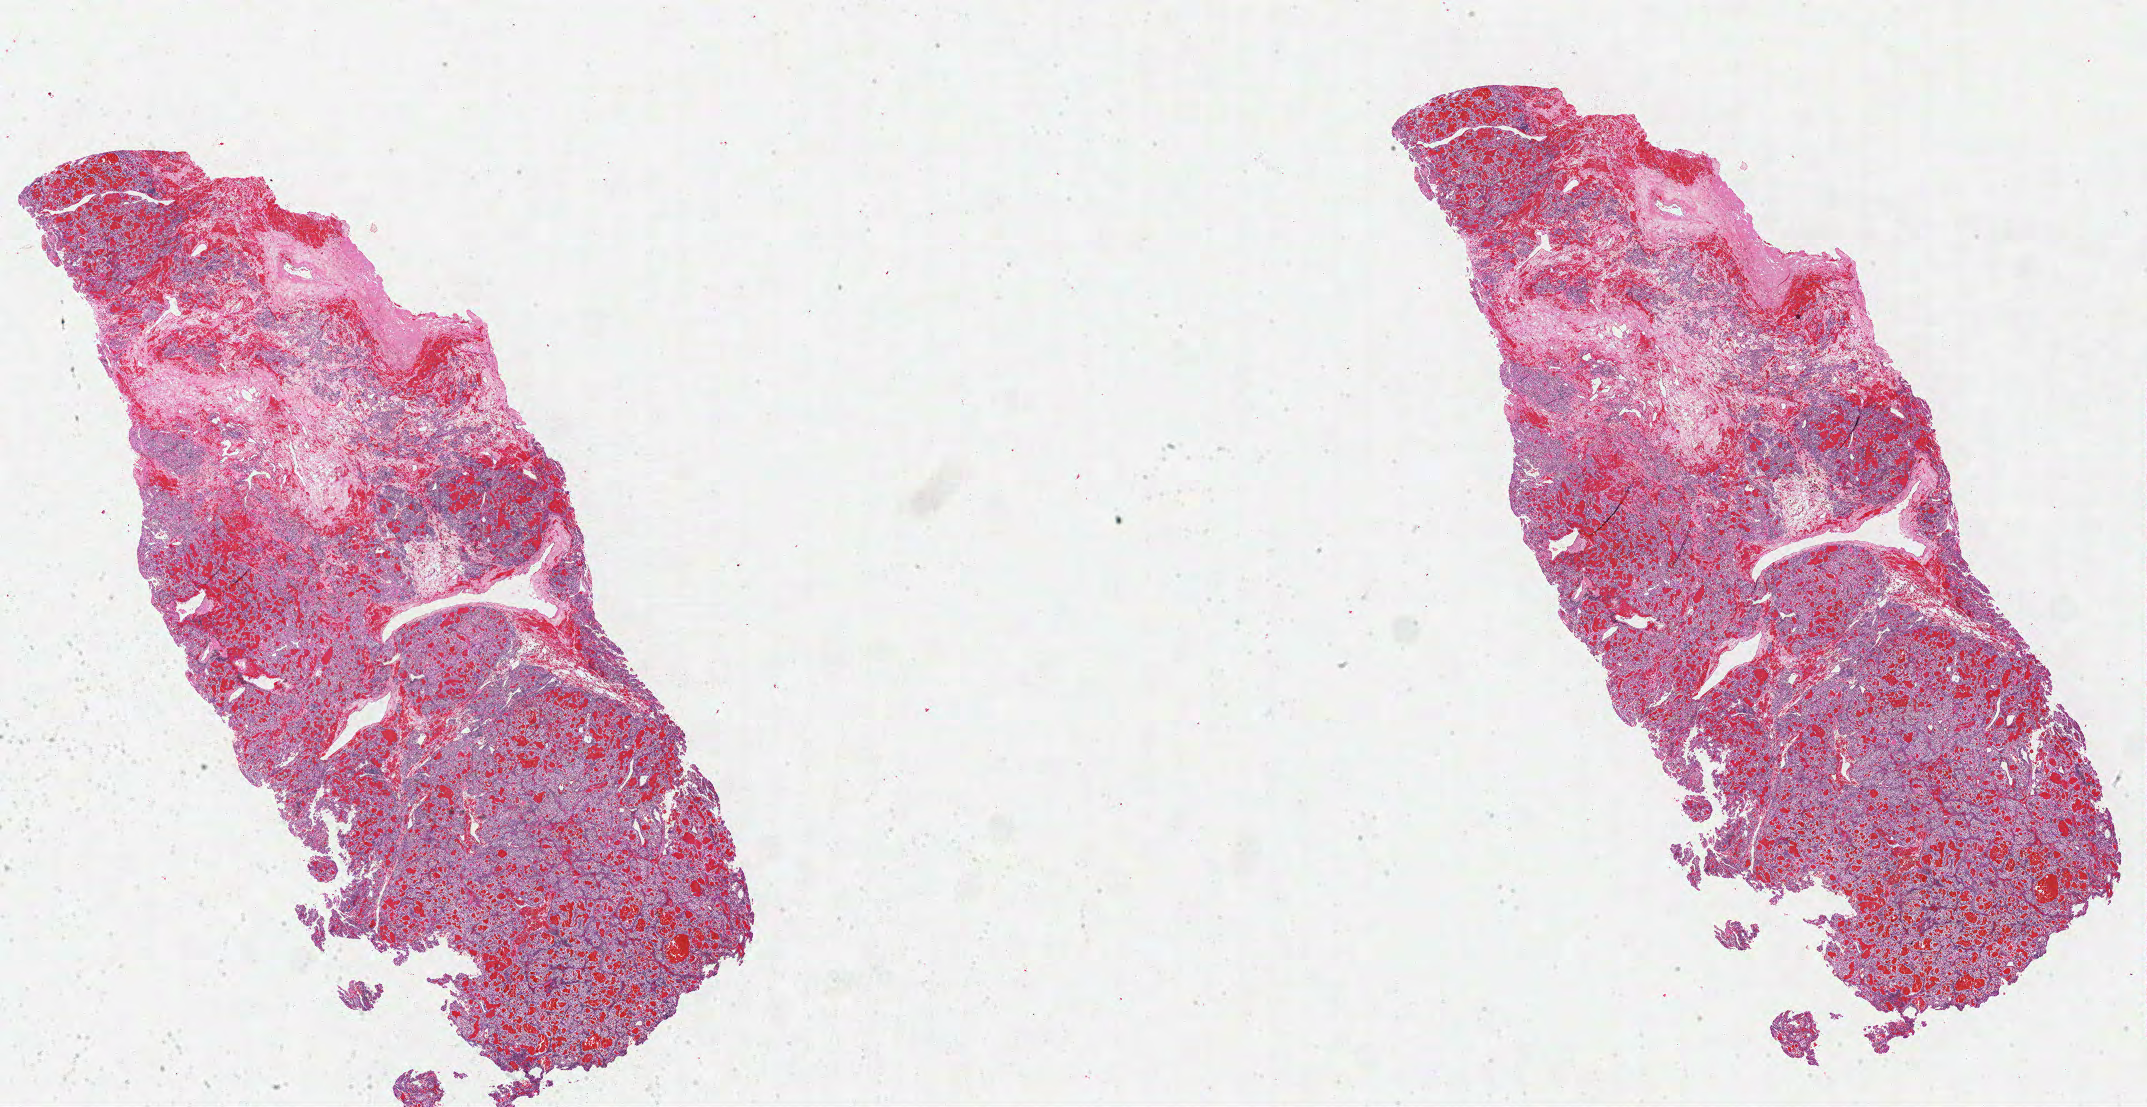
Whole-slide histology image, Hematoxylin and eosin (H&E) stained, whole scanned area (about 33.8 x 17.4 mm, slide scanned at 40x) shown as a low-resolution overview; formalin-fixed paraffin-embedded (FFPE) diagnostic section; primary tumour sample from the kidney. Patient: male, age at initial diagnosis 53 years. Histologic grade: G3 (poorly differentiated).
Laterality: right. Diagnosis: Clear cell adenocarcinoma, NOS. AJCC pathologic stage: I.